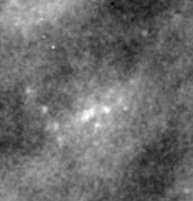
Crop from a digitized film mammogram around one marked abnormality, left breast, CC view, BI-RADS breast density category 4 (scale 1–4).
Marked abnormality: calcifications, morphology pleomorphic, distribution clustered; BI-RADS assessment category 4; subtlety rating 3 on a 1 (subtle) to 5 (obvious) scale; pathology result (as recorded, not read from the image): malignant.